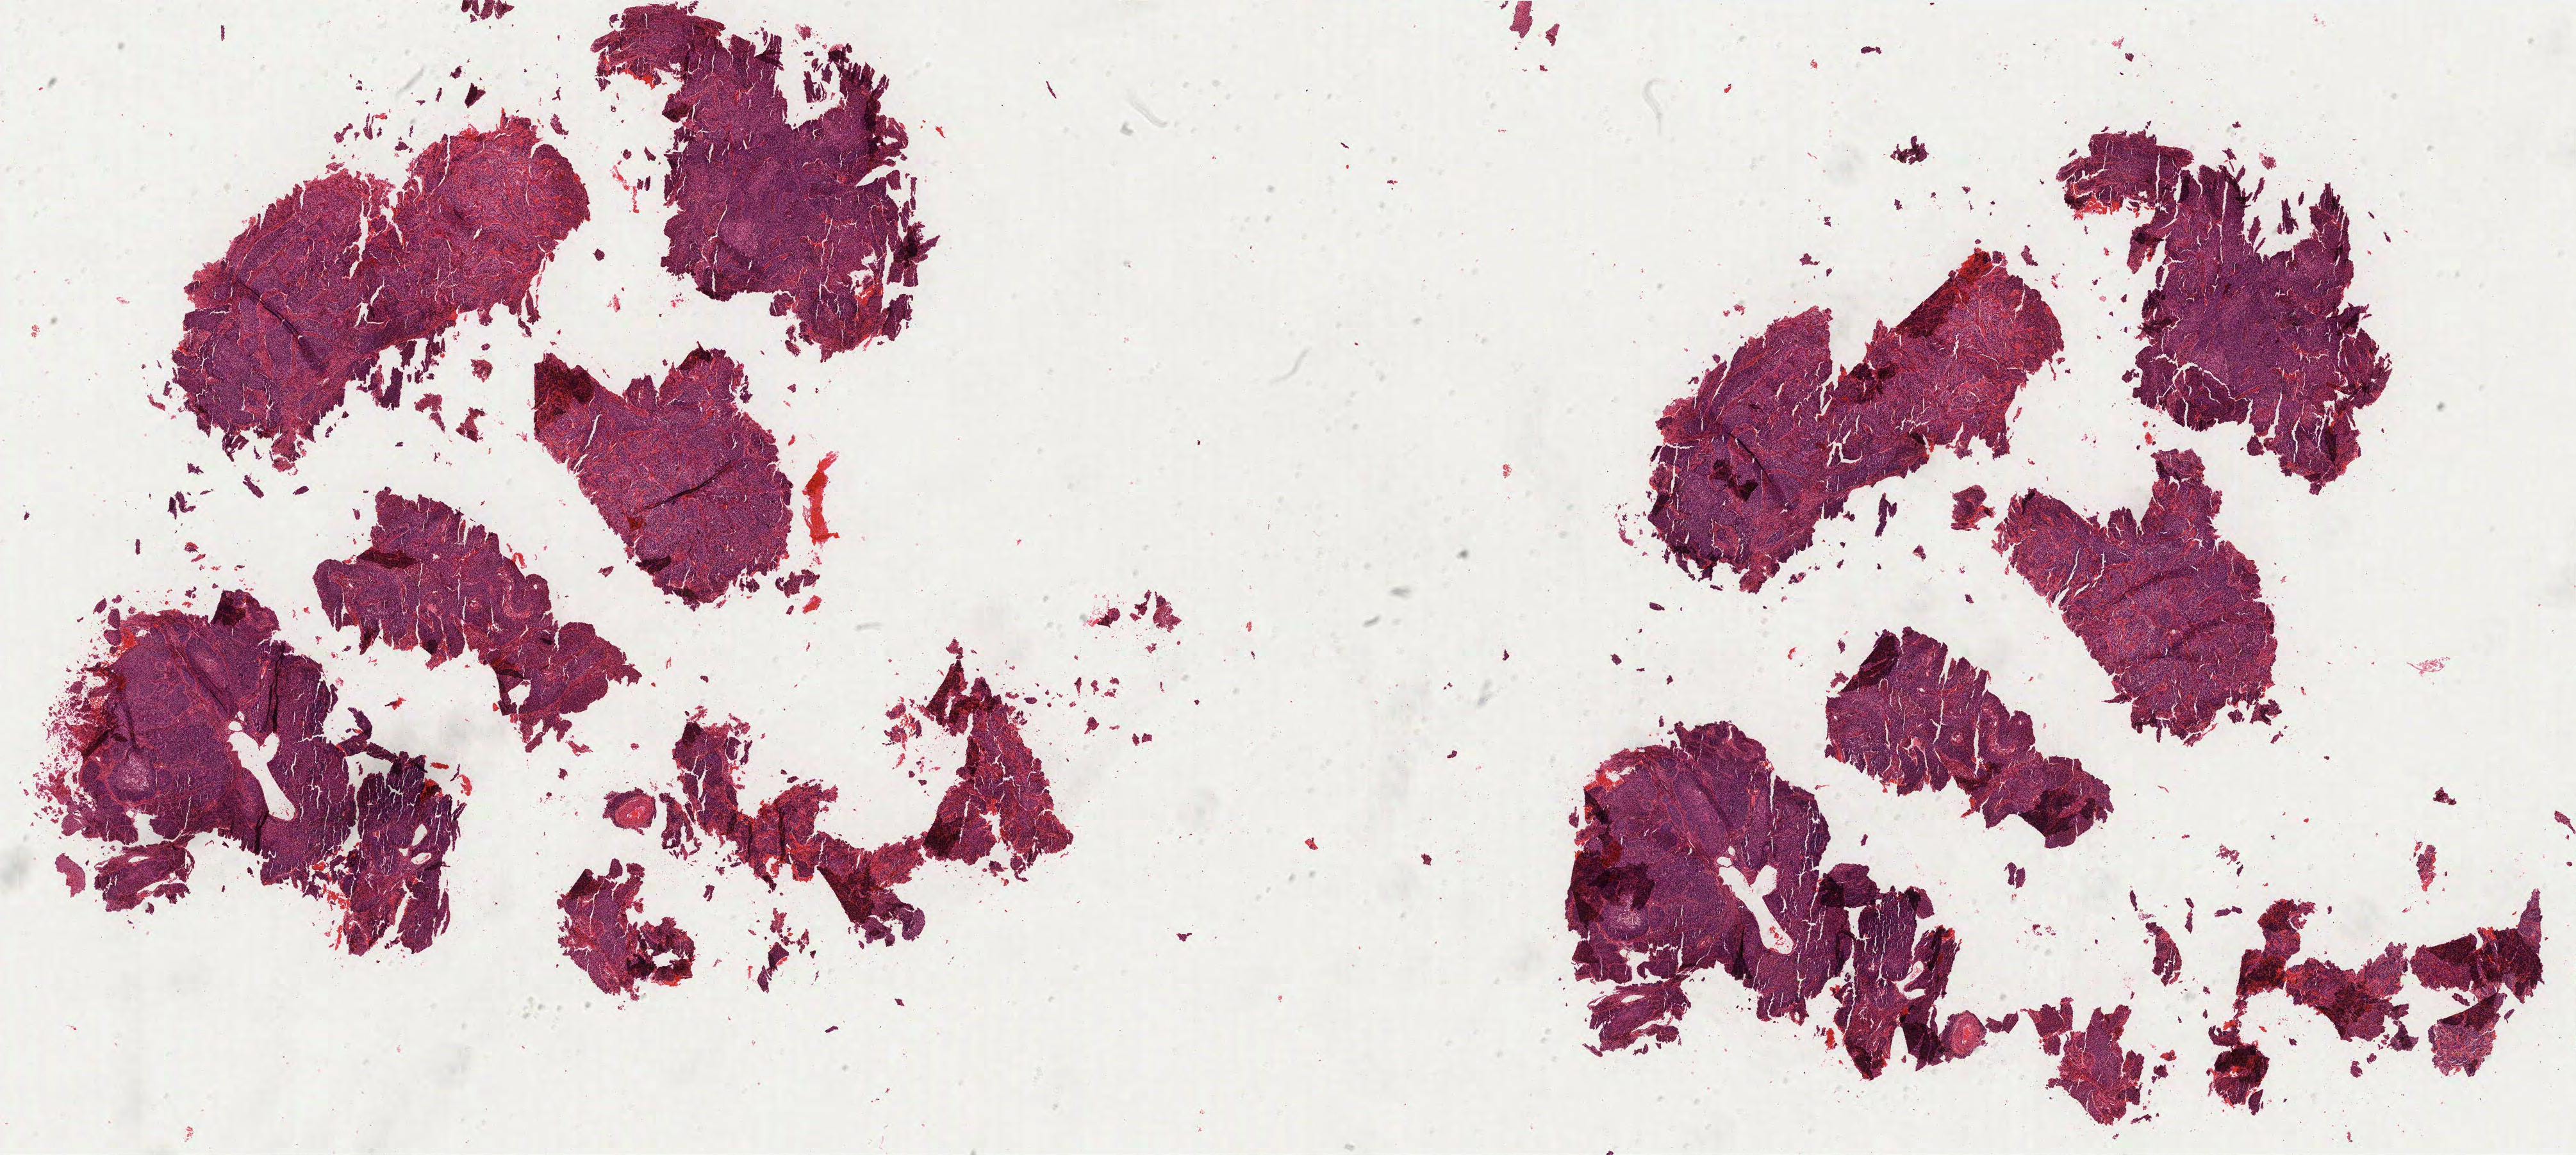
Whole-slide histology image, H&E-stained — a low-resolution overview of the entire scanned area, about 32.2 x 14.4 mm; formalin-fixed paraffin-embedded (FFPE) diagnostic section; cervix, primary tumour sample. Female, age 49 years at initial diagnosis. Histologic grade: G2 (moderately differentiated).
- diagnosis: Squamous cell carcinoma, NOS (cervix uteri)
- FIGO stage: IB2
- lymph nodes positive (case pathology): 0 of 40 examined